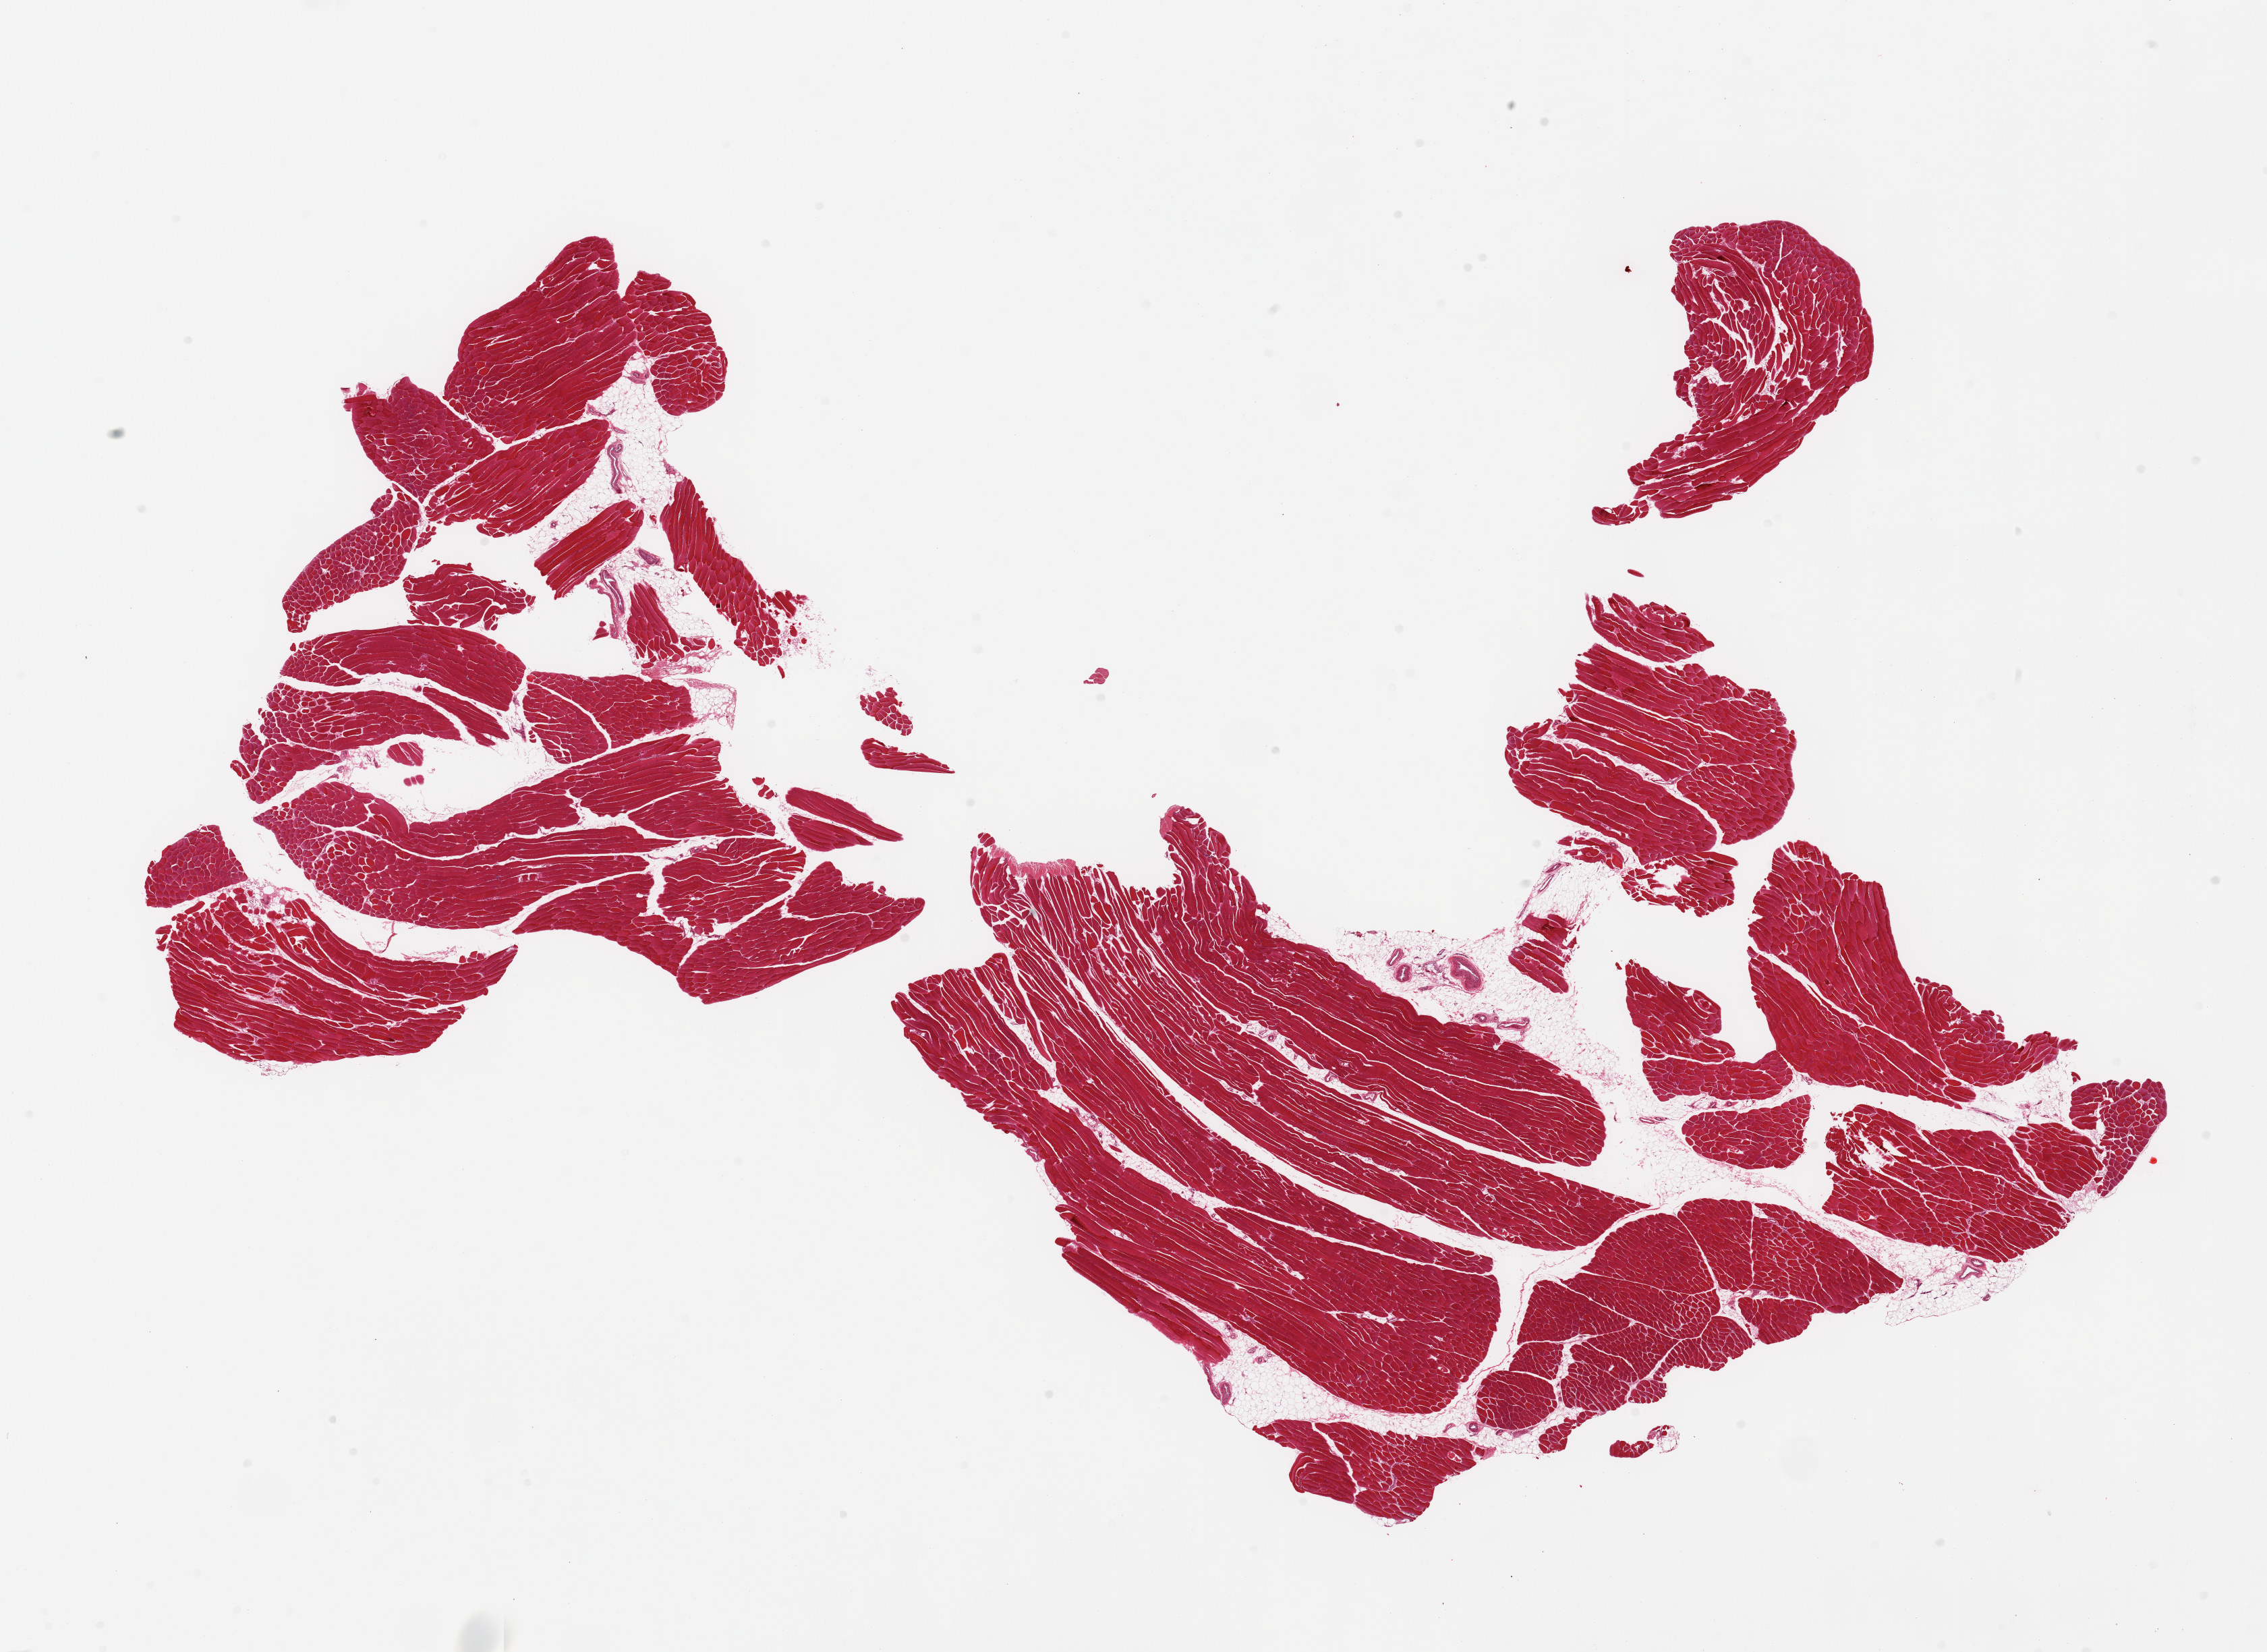
Whole-slide image, hematoxylin and eosin (H&E) stain — a low-resolution overview of the entire scanned area, about 26.6 x 19.4 mm (acquisition: 20x scan), PAXgene-fixed paraffin-embedded (PFPE) section, sampled site (target tissue): skeletal muscle, tissue donor sample. Male donor.
Reviewer comment on this tissue sample: 2 pieces, ~10% interstitial fat.